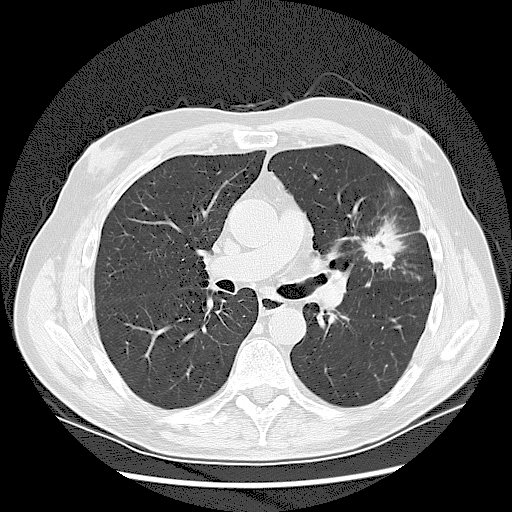
Low-dose screening chest CT, one axial slice. Reconstruction kernel LUNG. Lung window (W 1500 / L -600 HU). 2.5 mm slice thickness. 512 × 512 image matrix, field of view 380 × 380 mm.
Annotated regions visible in this slice (manually delineated by an expert):
- lesion 1 (tumor, upper lobe of left lung): bounding box (x1, y1, x2, y2) in pixels: (368, 224, 399, 264)